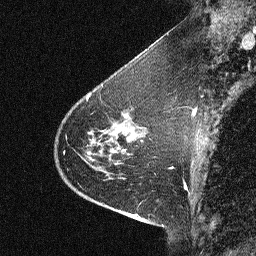
Breast MRI (dynamic contrast-enhanced), one sagittal slice; slice 17 of 64 in the series (ordered by position); dynamic contrast-enhanced study with each time point stored as its own series, time point 2 of 3 at this slice position (early post-contrast, ordered by acquisition time); 1.5 T; TE 4.5 ms, TR 11 ms; 256 × 256 image matrix, field of view 200 × 200 mm. Patient: female, 46 years. From the clinical record (not read from this slice): setting: breast cancer imaged before/during neoadjuvant chemotherapy; receptor status: HER2-positive.
Outlined on this slice (semi-automatic segmentation, software-assisted and operator-edited):
- analysis volume of interest (the breast-tissue region the enhancement analysis was run in; not a lesion): box from (x=42, y=80) to (x=150, y=180) px
- tumour enhancement mask (voxels above the 90 % enhancement threshold inside the analysis volume of interest): (x=88, y=115)–(x=128, y=162)